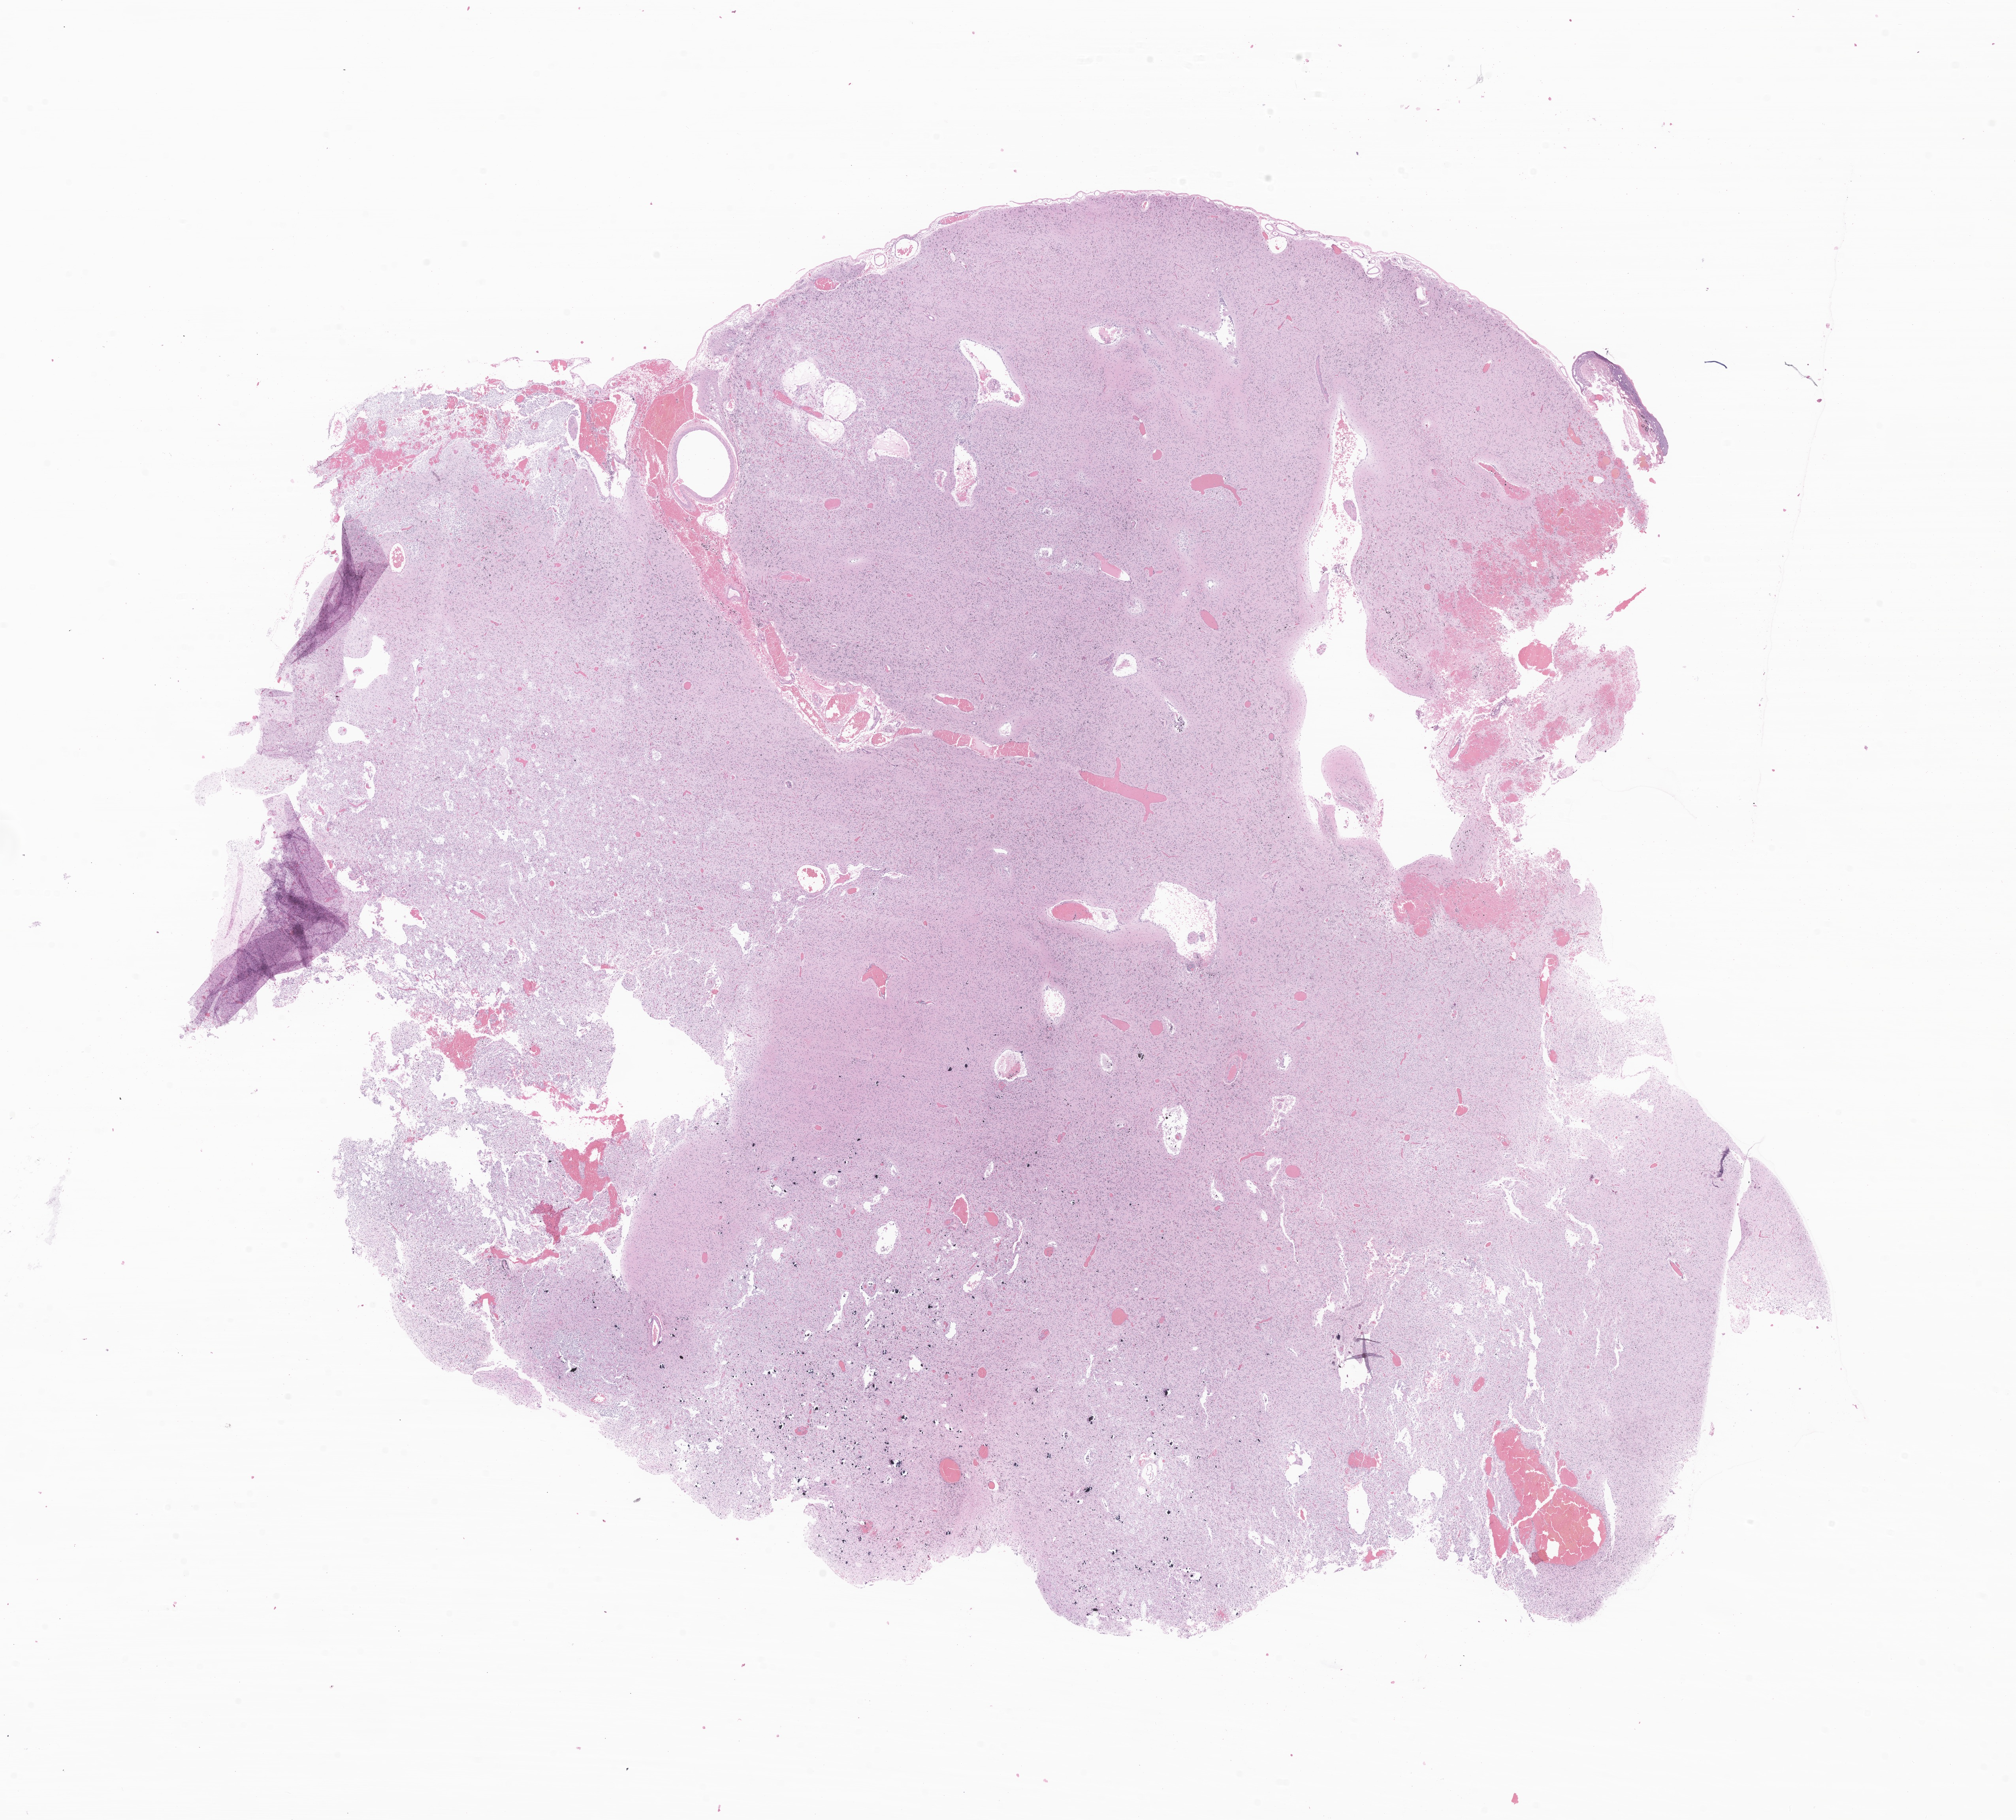
Hematoxylin and eosin (H&E) whole-slide image of tumor tissue from the brain stem, a low-resolution overview of the entire scanned area, about 21.5 x 19.4 mm, formalin-fixed, paraffin-embedded (FFPE) tissue. Patient male; age 191 months (15 years 11 months).
• recorded diagnosis: Ganglioglioma, NOS